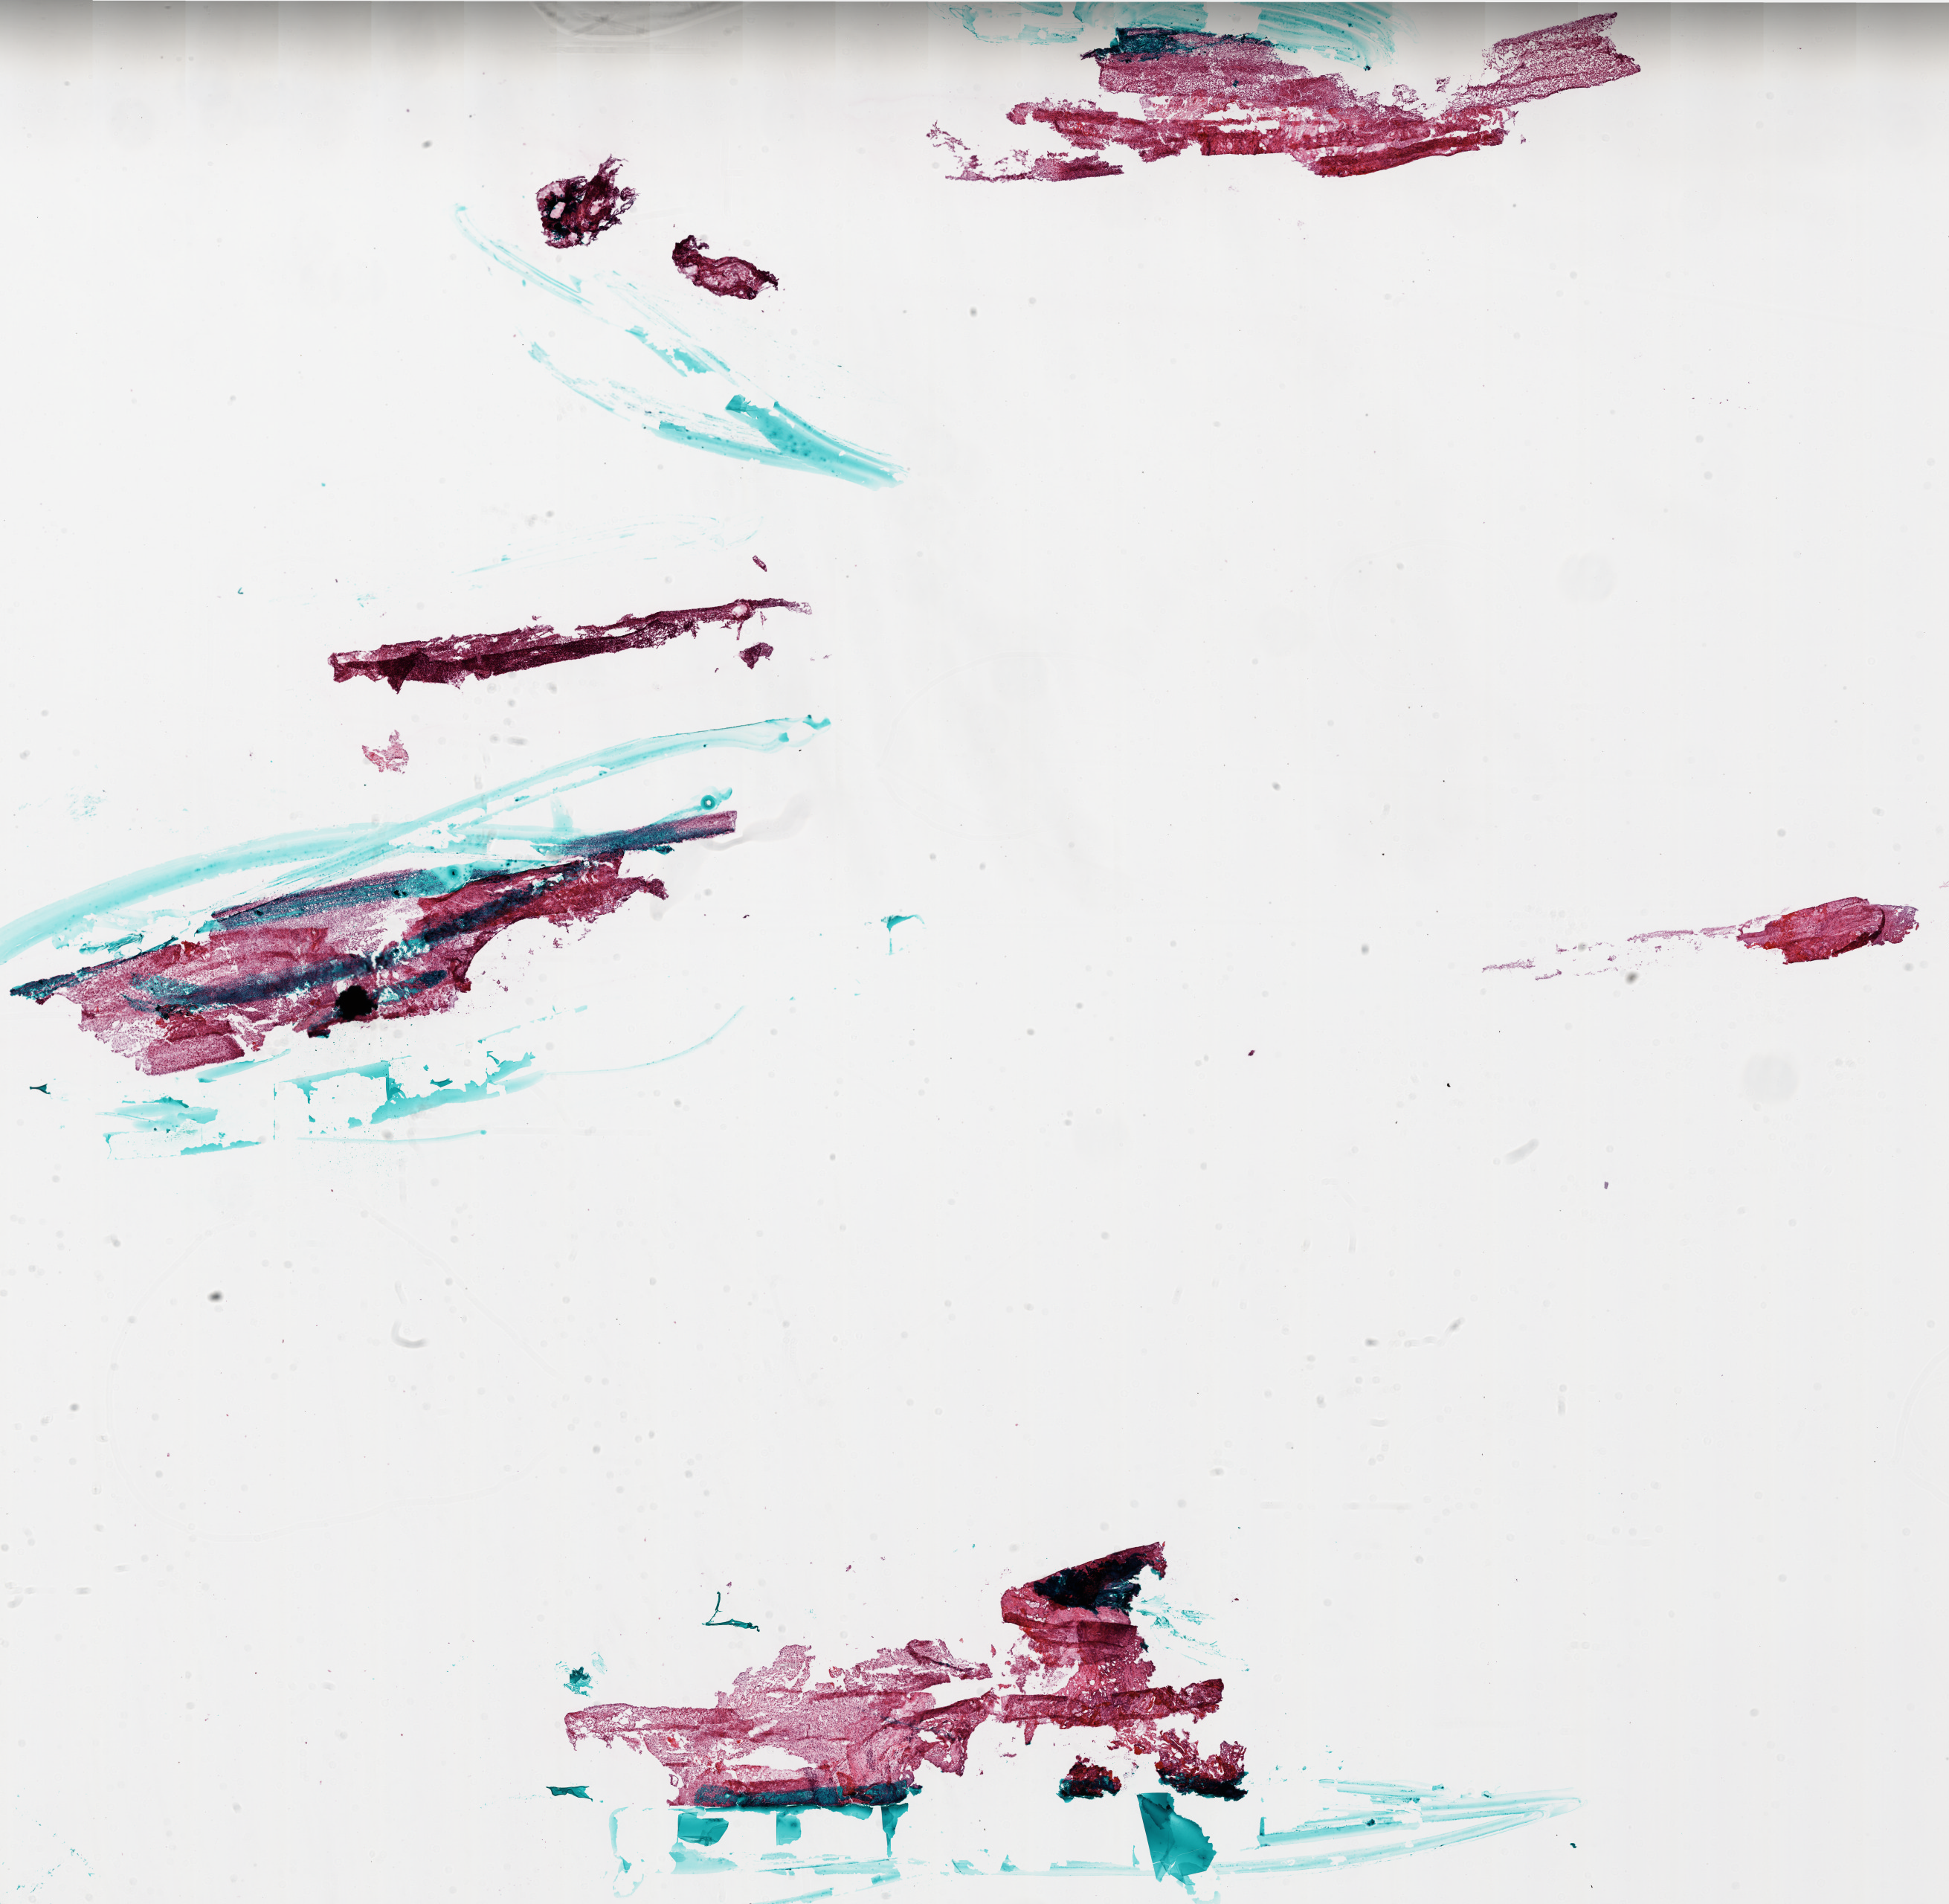
Digitized H&E-stained tissue section (whole slide), whole scanned area (about 21.0 x 20.5 mm) shown as a low-resolution overview. Frozen section from the bottom of the tissue portion. Sample: primary tumour, brain. Female patient; age at initial diagnosis 43 years.
Diagnosis: Glioblastoma.